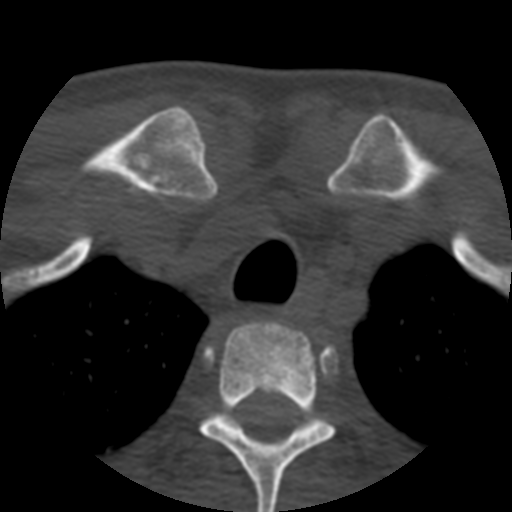
CT including the spine, one axial slice; slice 429 of 508 in the series (ordered by position); reconstruction kernel STANDARD; 120 kVp; bone window (W 1800 / L 400 HU); 1.25 mm slice thickness; 512 × 512 image matrix, field of view 160 × 160 mm. Patient age 57 years. Case-level facts recorded for this patient, not image findings: primary cancer: prostate.
Structures marked on this image (semi-automatically segmented with operator editing):
- T2 vertebra: bounding box (x1, y1, x2, y2) in pixels: (199, 322, 336, 512)
- T3 vertebra: (325, 420, 332, 426)